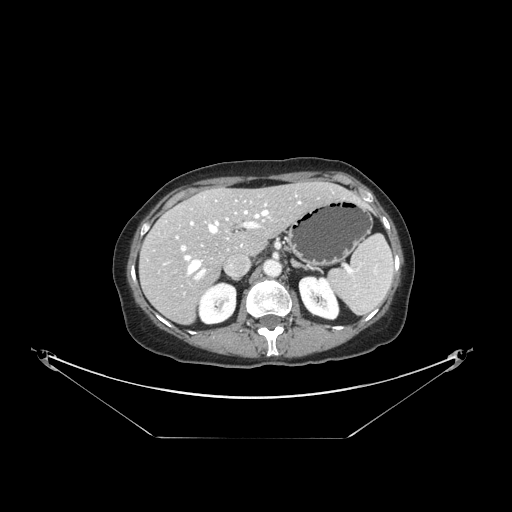
Contrast-enhanced abdominal CT, one axial slice. Position 95 of 148 along the scan axis. 120 kVp. Intravenous contrast given. Soft-tissue window (W 400 / L 40 HU). 2.5 mm slice thickness. 512 × 512 image matrix. Female patient, age 73 years. From the clinical record (not read from this slice): diagnosis: colorectal cancer liver metastases, imaged before liver resection; multiple liver metastases: no; largest metastasis: 1 cm.
Structures marked on this image (outlined manually by an expert reader):
- hepatic veins: bounding box (x1, y1, x2, y2) in pixels: (184, 195, 300, 274)
- liver: (141, 182, 353, 323)
- planned liver remnant (the part of the liver to remain after resection): (169, 183, 354, 255)
- portal vein (with intrahepatic branches): (176, 204, 267, 280)